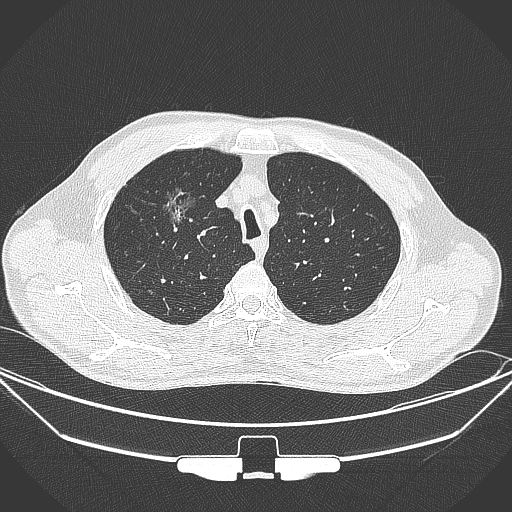
Chest CT, one axial slice; 120 kVp; lung window (W 1500 / L -600 HU); 1 mm slice thickness; 512 × 512 image matrix, field of view 399 × 399 mm. Male patient, age 67 years. Case-level facts recorded for this patient, not image findings: clinical TNM (as recorded): T1c N0 M0.
Structures marked on this image (bounding box drawn by a radiologist):
- lung tumour (recorded histology: adenocarcinoma): bounding box [x1, y1, x2, y2] px = [151, 180, 201, 236]